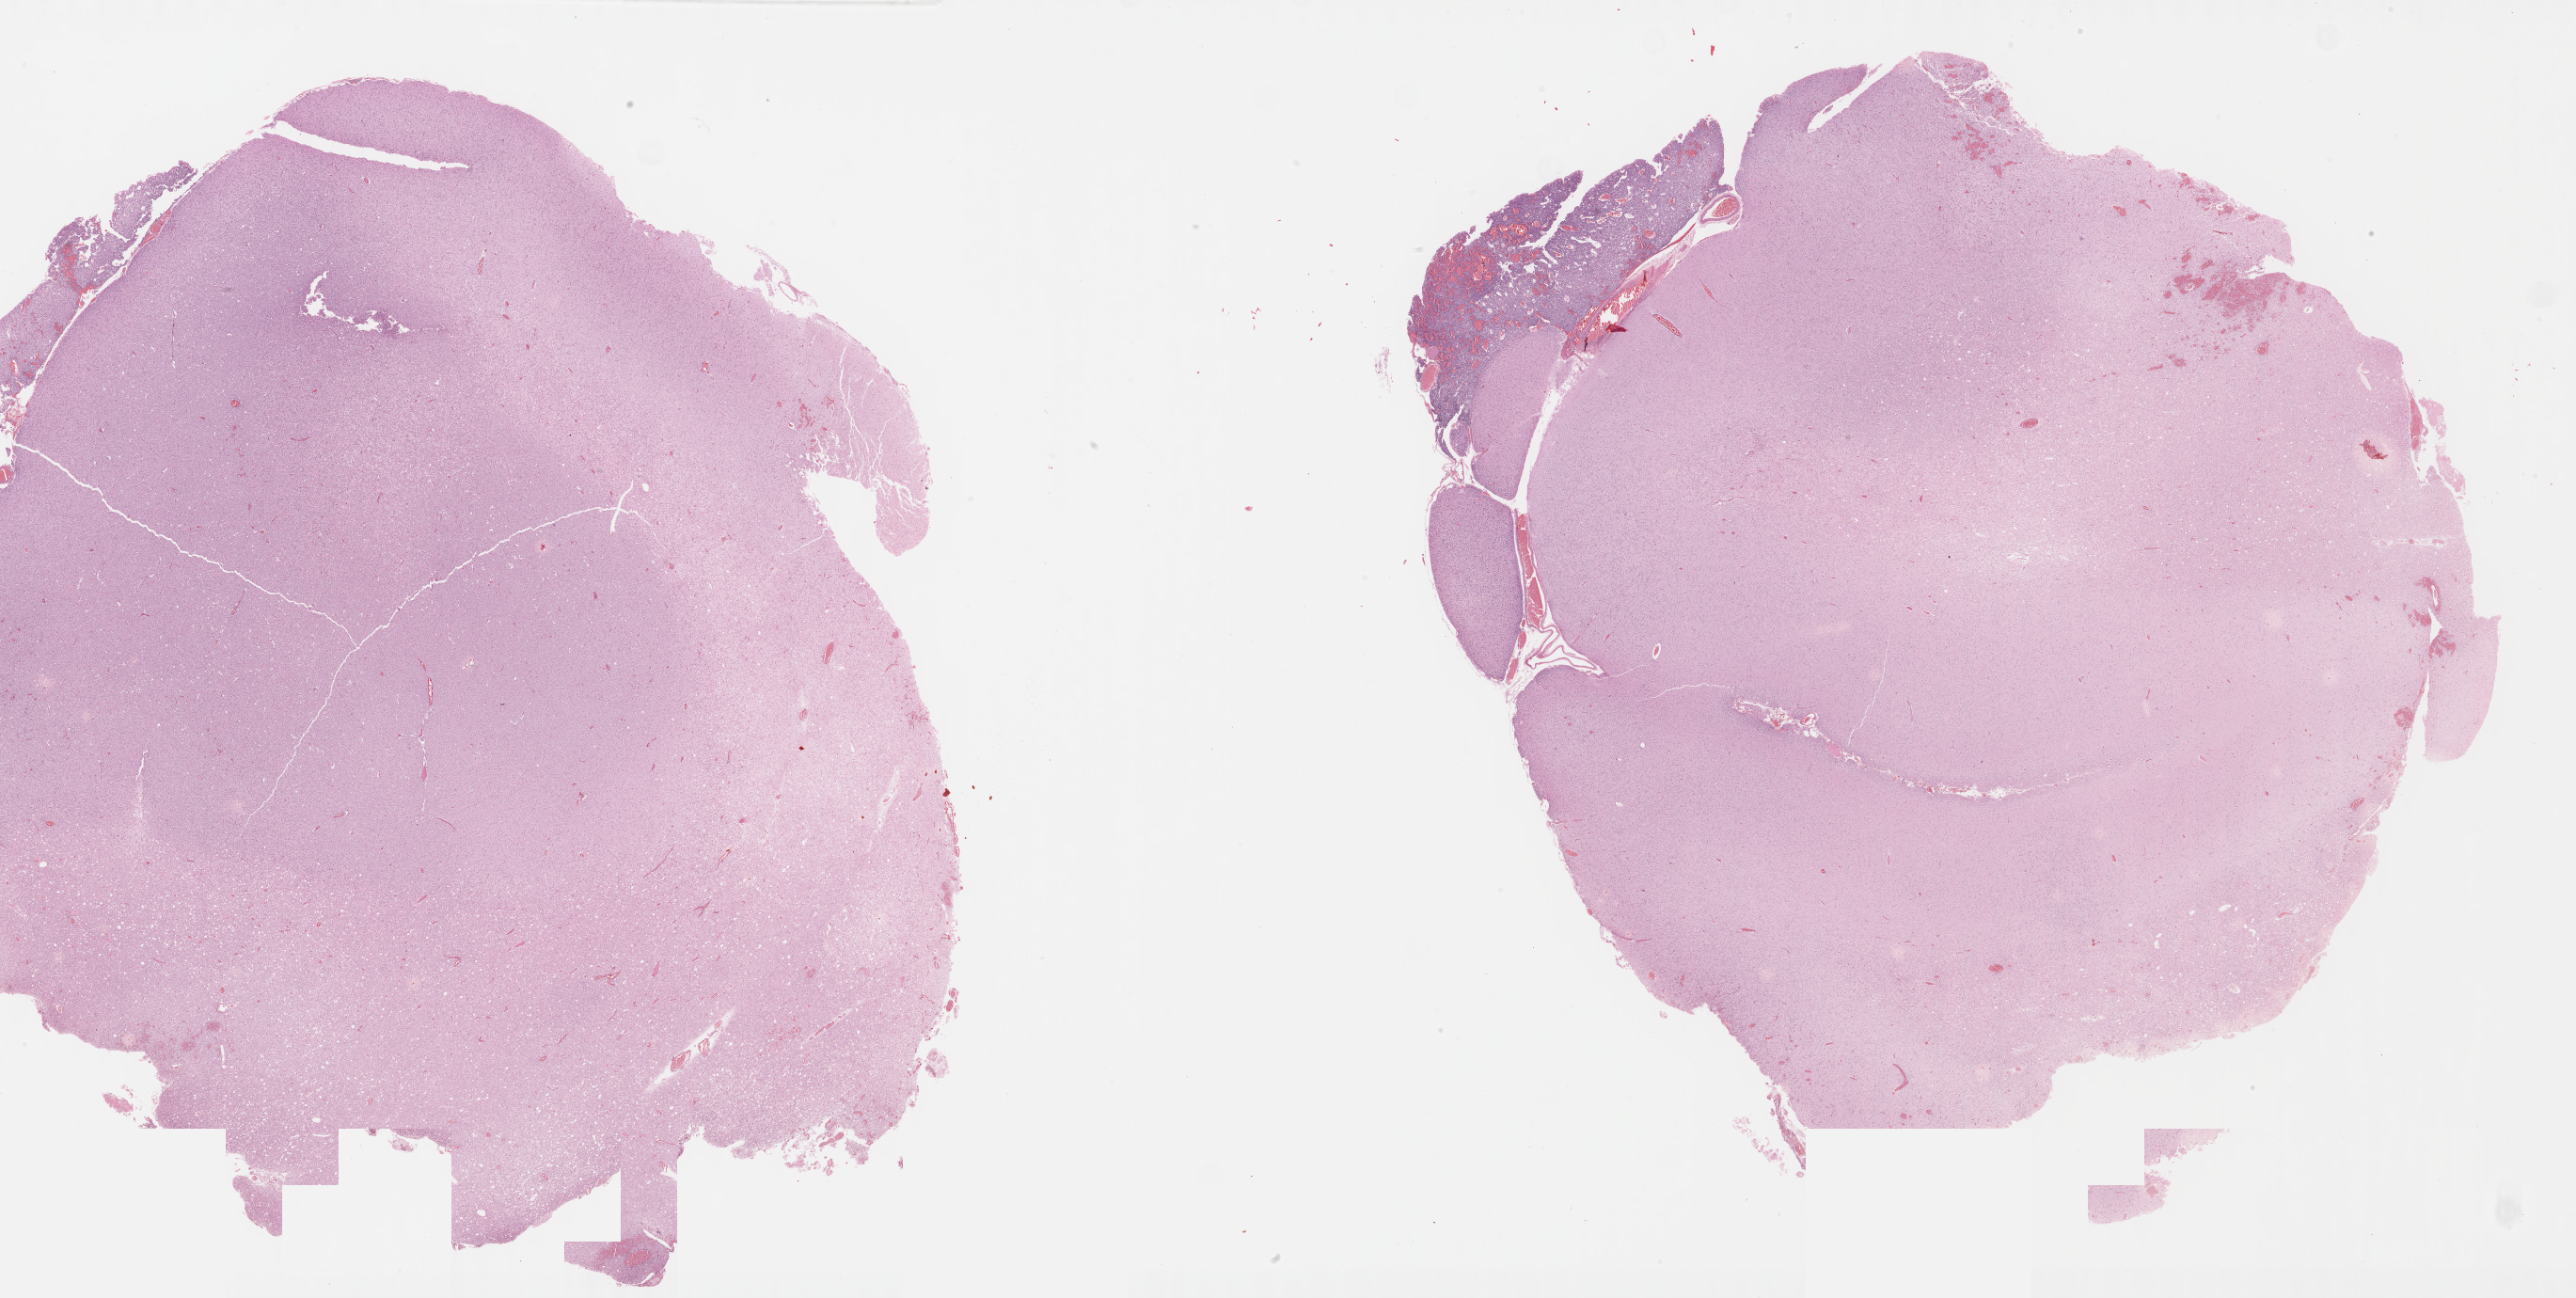
Whole-slide histology image, H&E, whole scanned area (about 44.3 x 22.3 mm, slide scanned at 40x) shown as a low-resolution overview. Formalin-fixed paraffin-embedded (FFPE) diagnostic section. Primary tumour sample from the brain. Female, age 38 years at initial diagnosis. Histologic grade: G2 (moderately differentiated).
Diagnosis: Oligodendroglioma, NOS (cerebrum).